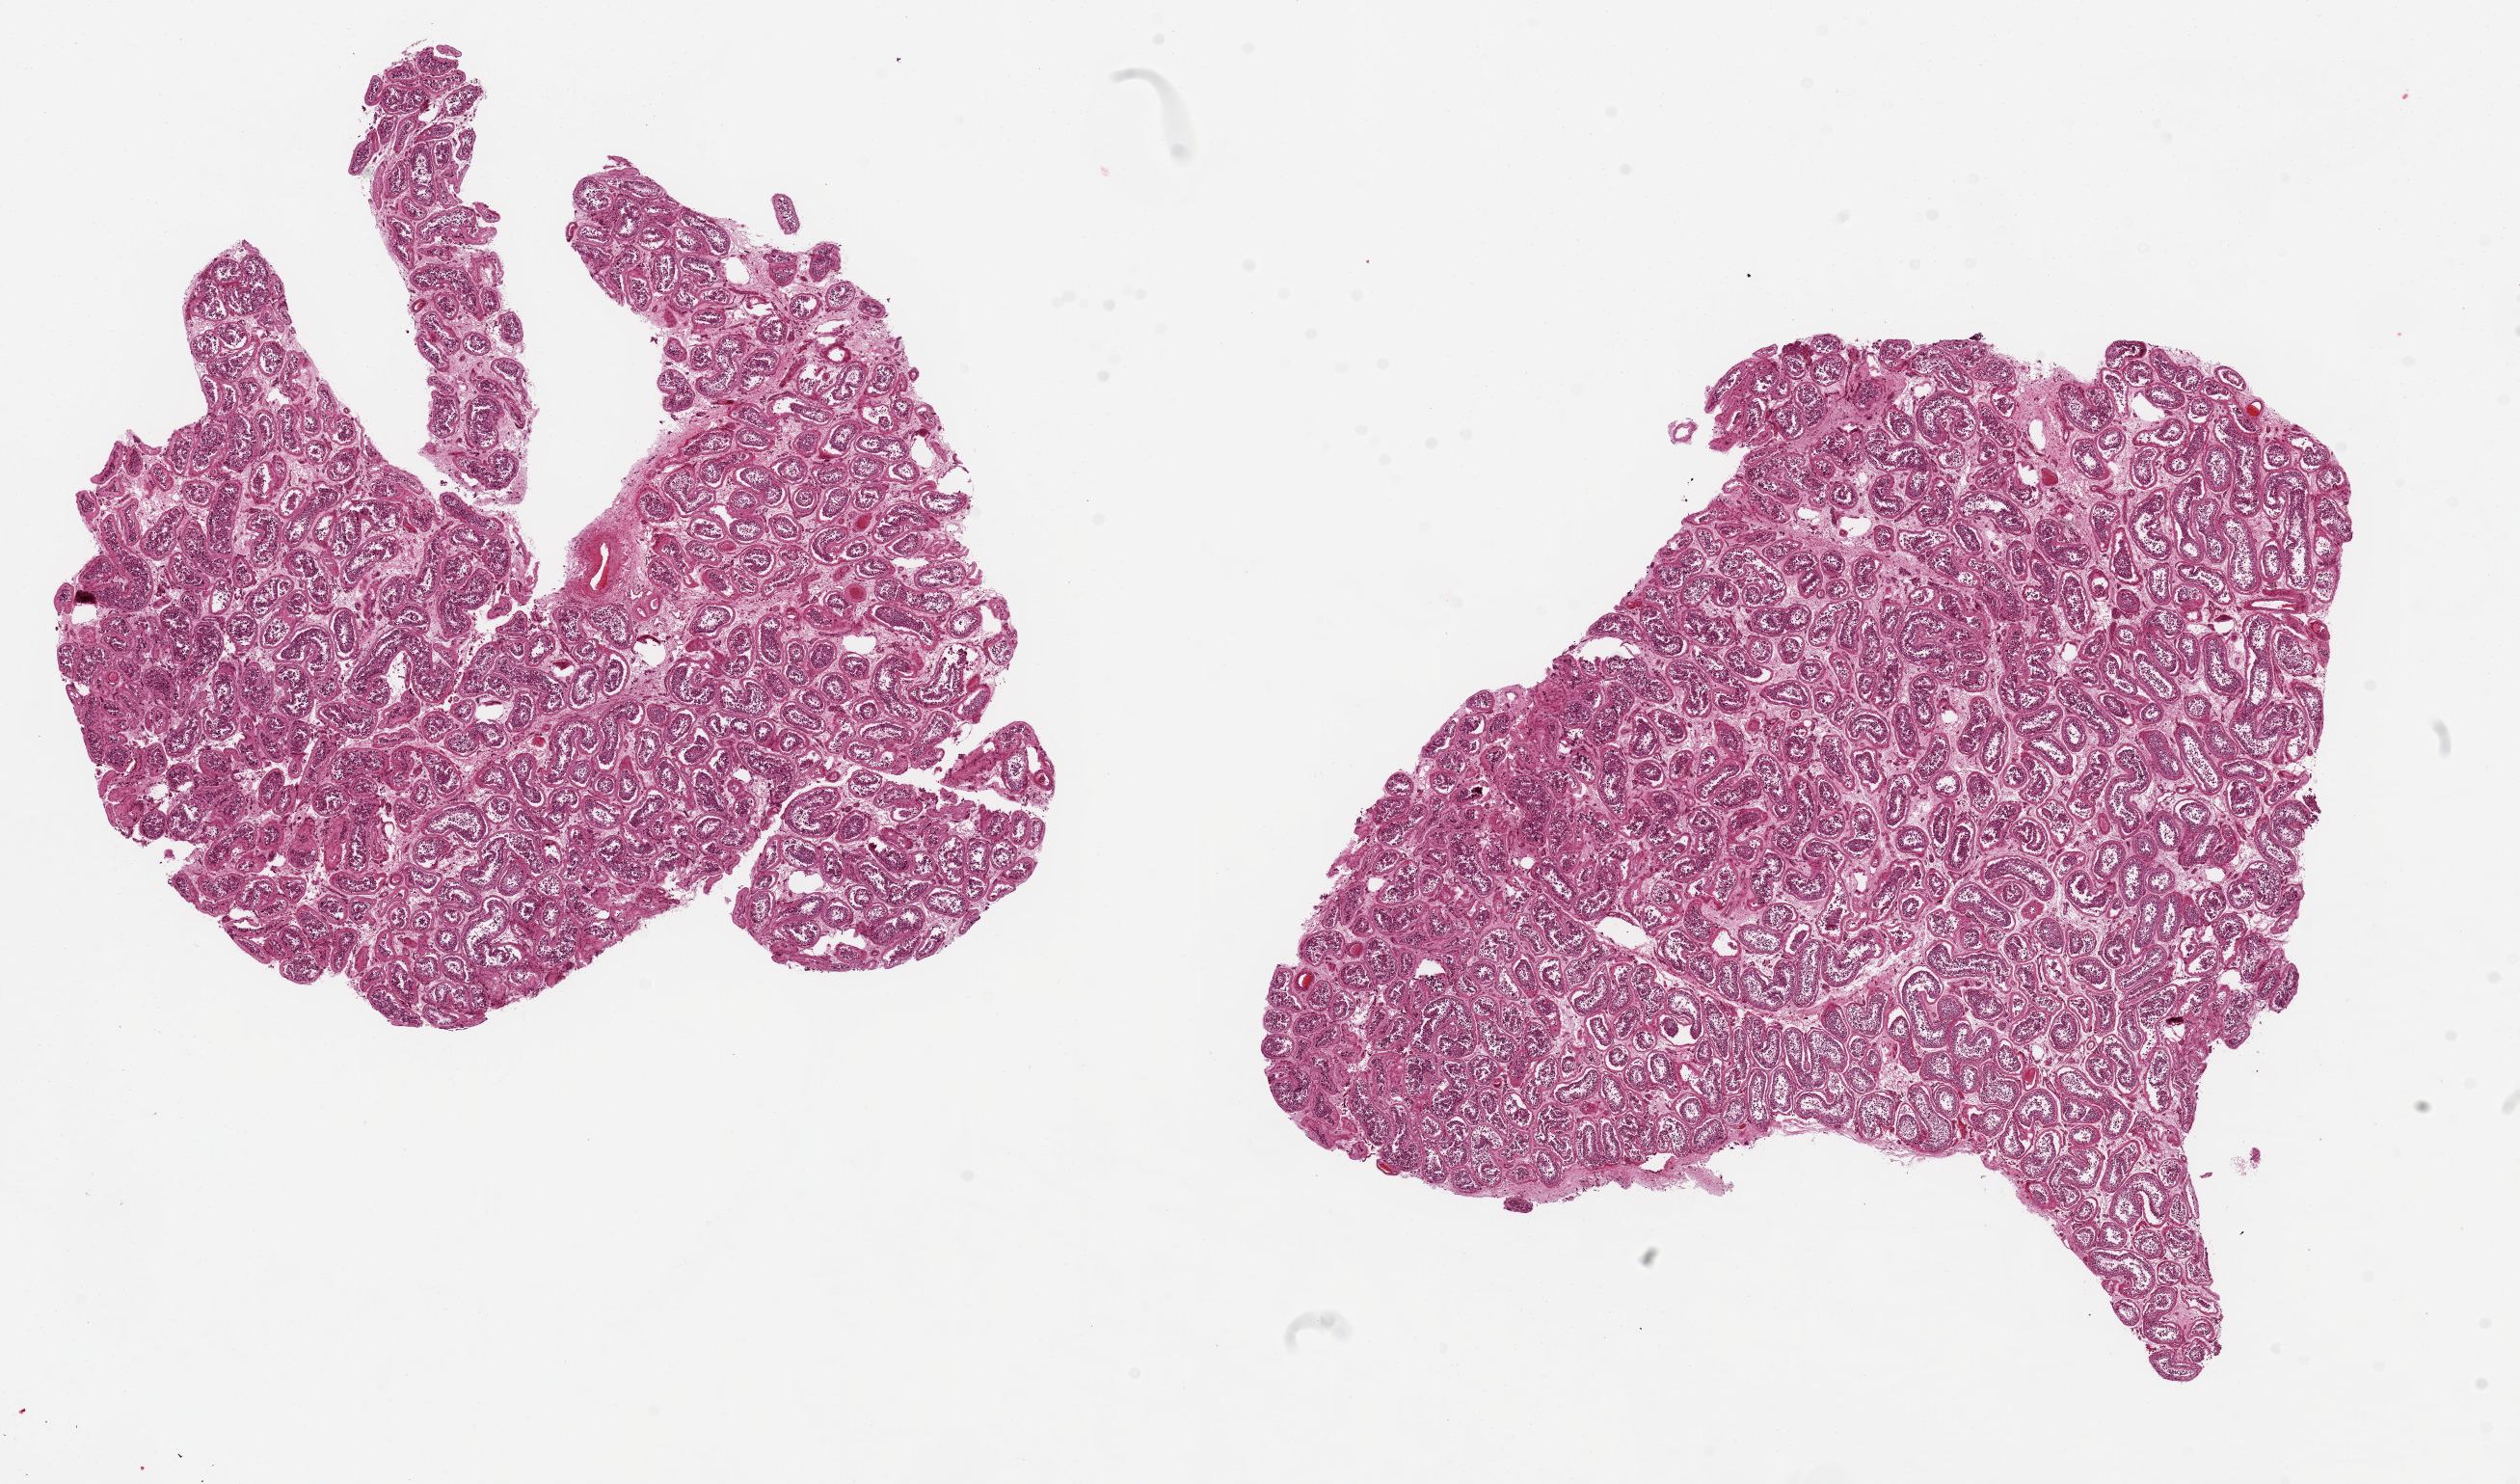
Whole-slide image, haematoxylin and eosin stain — shown as a low-resolution overview of the whole scanned area (about 20.7 x 12.2 mm, acquisition: 20x scan); PAXgene-fixed paraffin-embedded (PFPE) section; section of testis (target tissue); donor tissue sample. Donor sex: male.
Reviewer comment on this tissue sample: 2 aliquots, ~8x7mm. Spermatogenesis appears arrested.